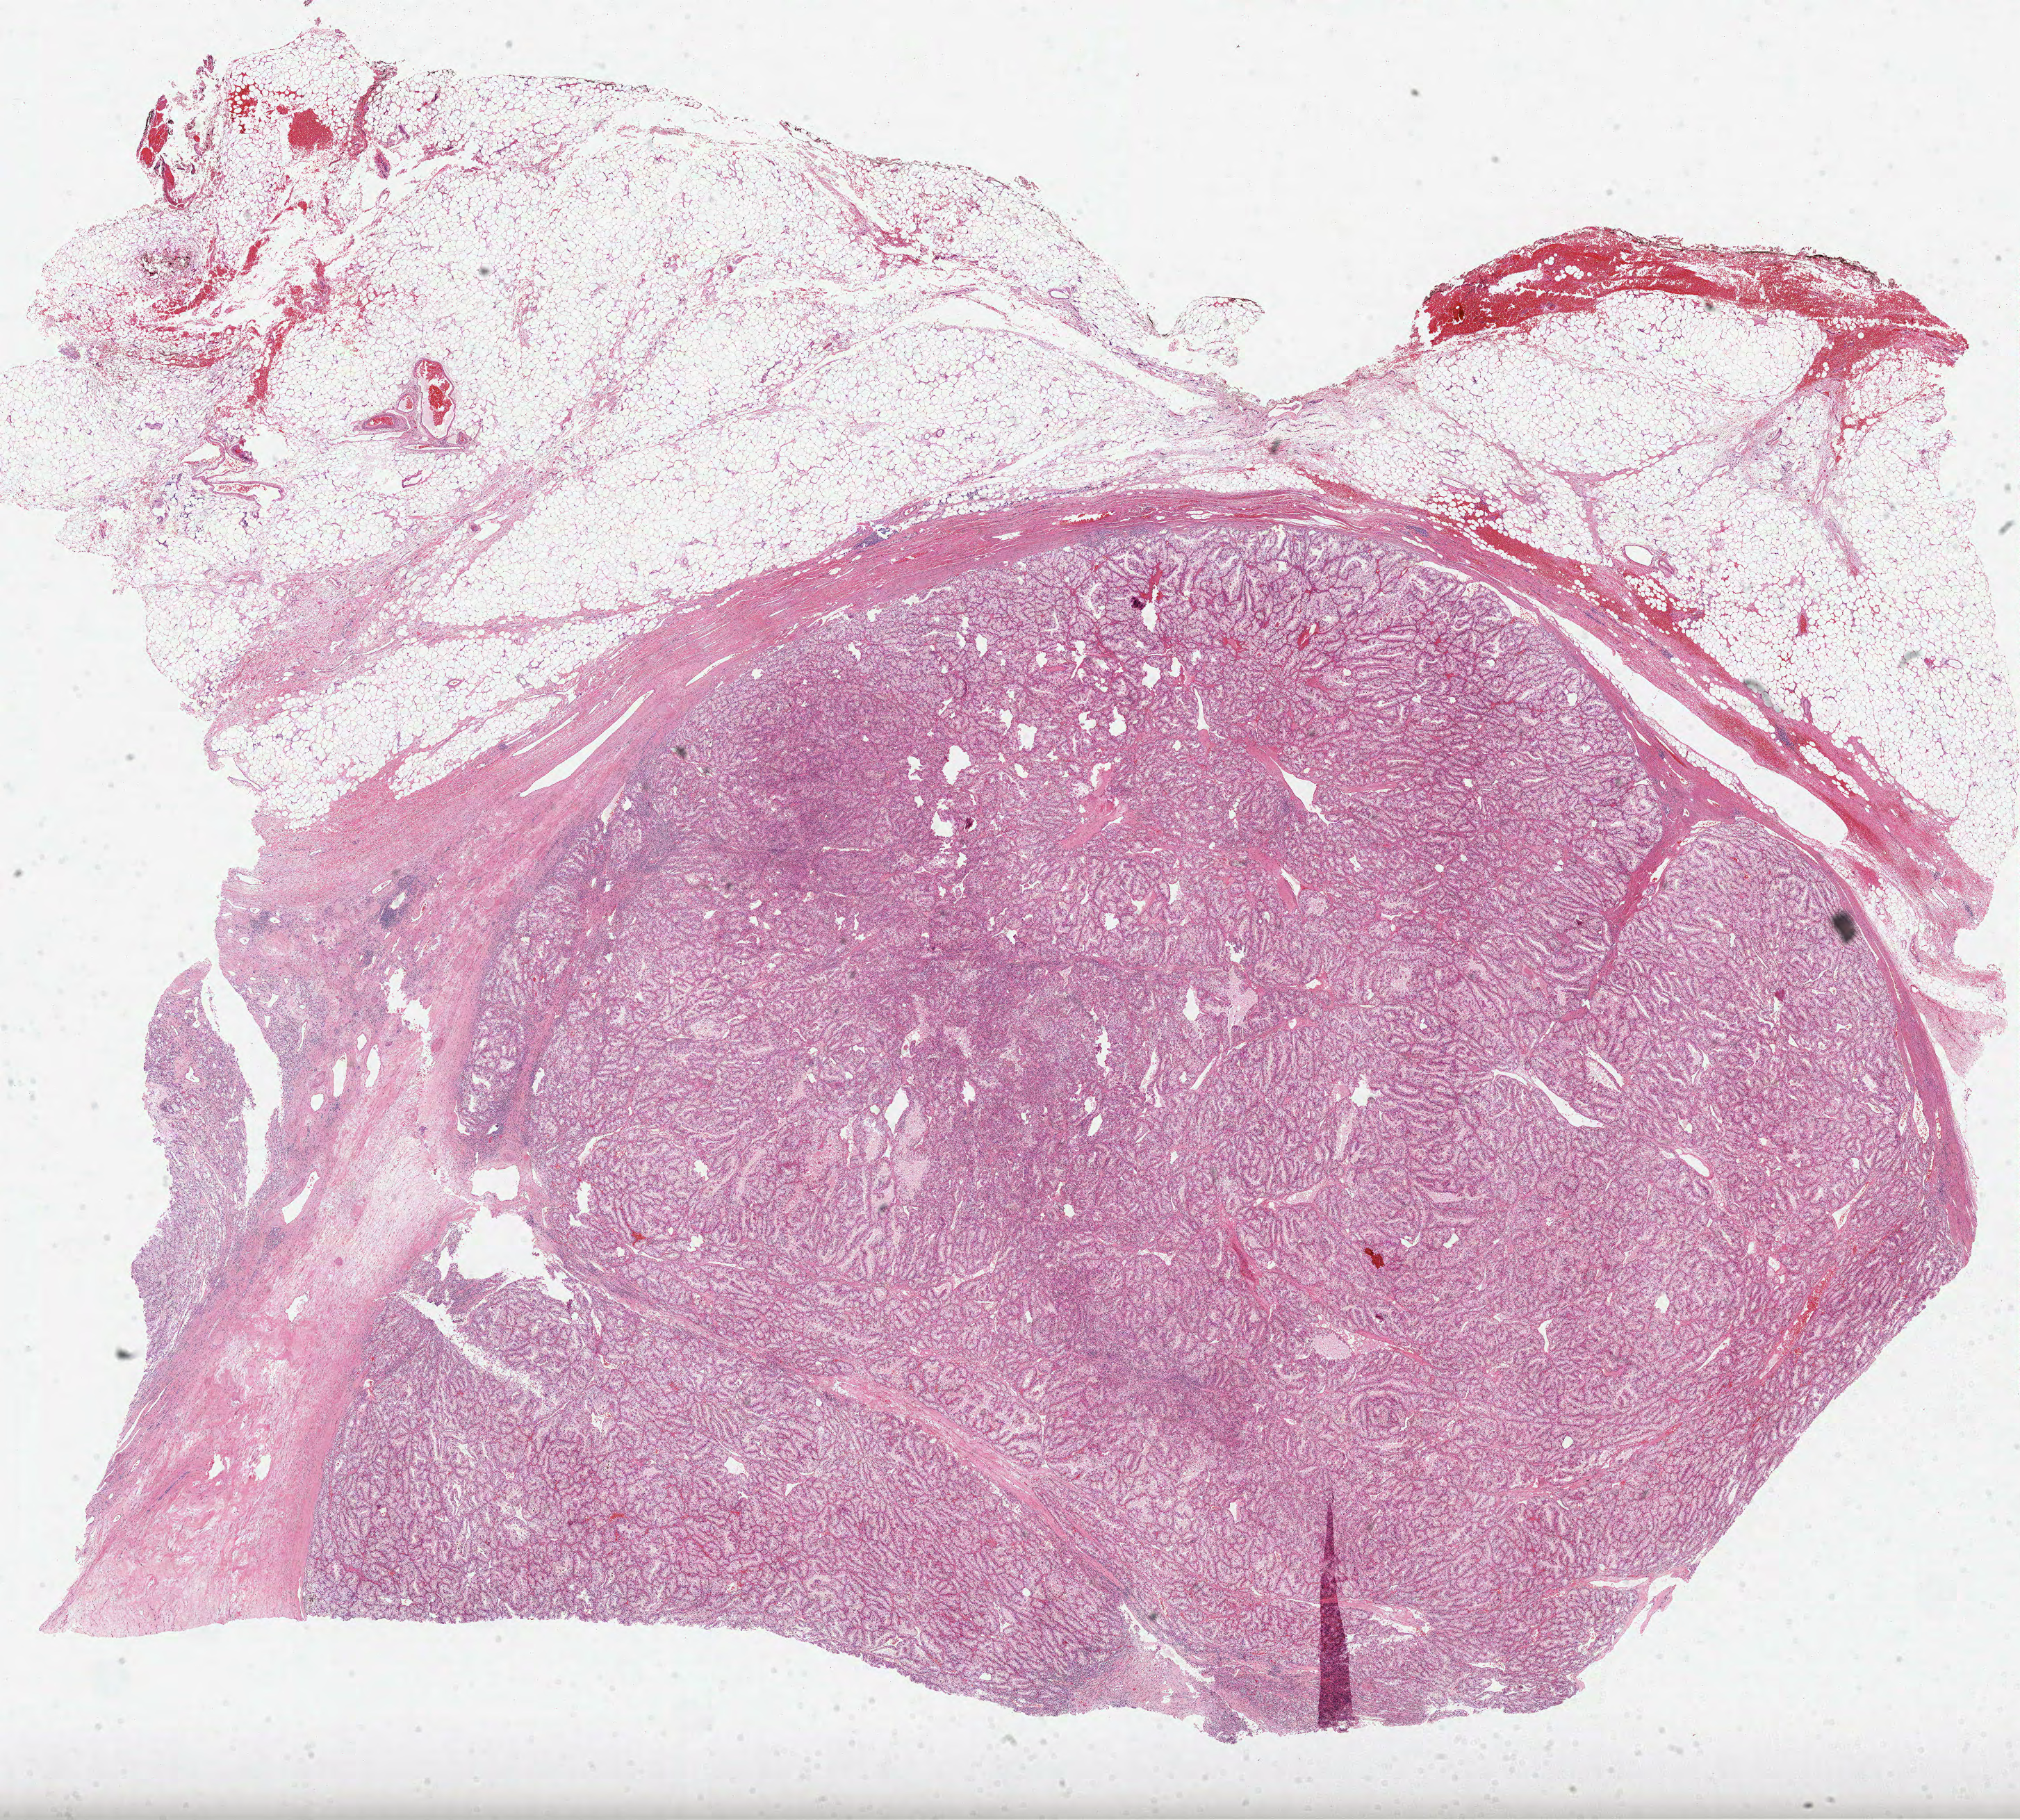
Whole-slide histology image, Hematoxylin and eosin (H&E) stained — shown as a low-resolution overview of the whole scanned area (about 23.4 x 21.1 mm, from a 40x scan), formalin-fixed paraffin-embedded (FFPE) diagnostic section, primary tumour sample from the kidney. Male, age 72 years at initial diagnosis. Histologic grade: G4 (undifferentiated).
AJCC pathologic stage: III. Diagnosis: Clear cell adenocarcinoma, NOS.